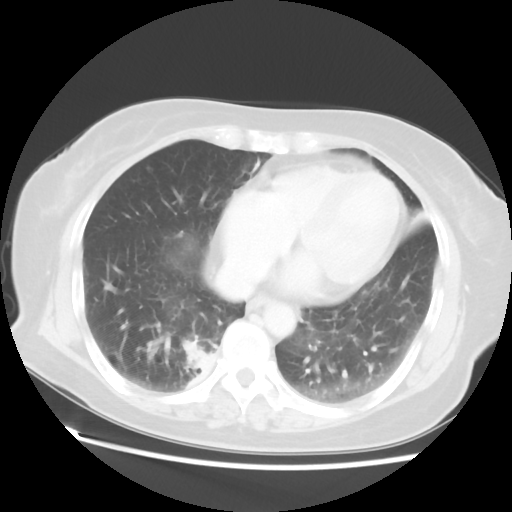
Chest CT, one axial slice; position 20 of 52 along the scan axis; reconstruction kernel STANDARD; 120 kVp; lung window (W 1500 / L -600 HU); 512 × 512 image matrix. Female patient, age 69 years. Case-level facts recorded for this patient, not image findings: clinical TNM (as recorded): T2 N1 M1a.
Structures marked on this image (rectangle marked by the reading radiologist):
- lung tumour (recorded histology: adenocarcinoma): box from (x=181, y=336) to (x=219, y=389) px